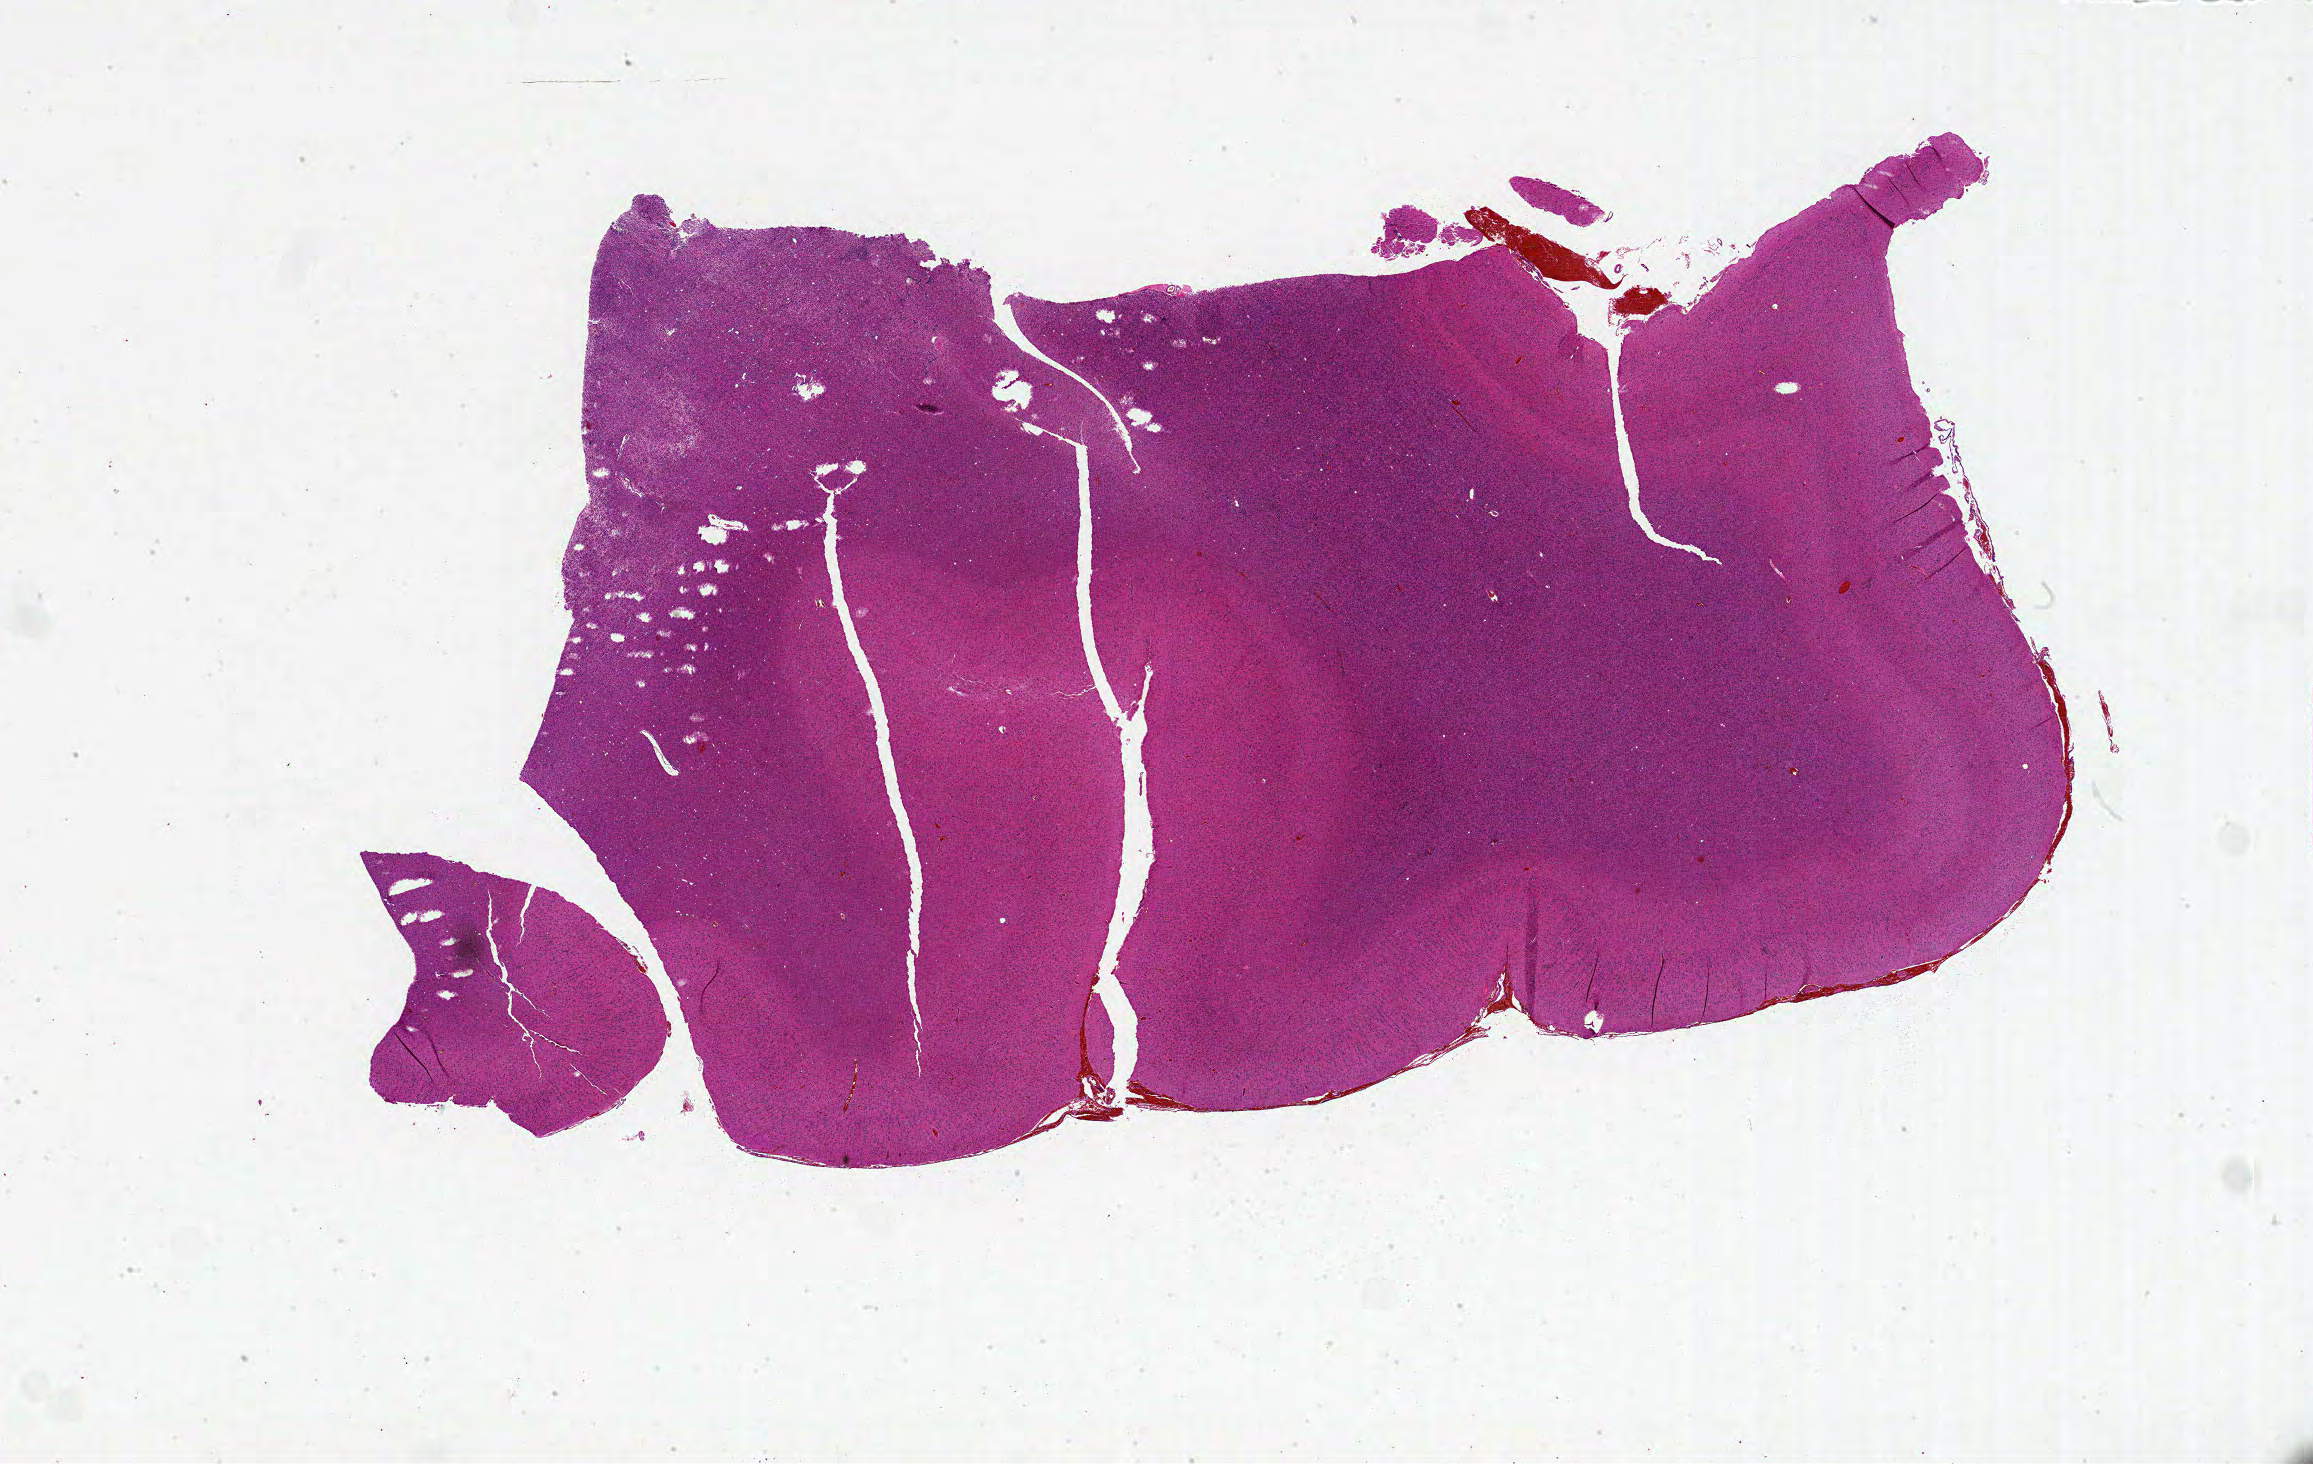
Whole-slide histology image, H&E-stained — shown as a low-resolution overview of the whole scanned area (about 37.0 x 23.4 mm, acquisition: 20x scan); formalin-fixed paraffin-embedded (FFPE) diagnostic section; brain, primary tumour sample. Male patient; age at initial diagnosis 77 years.
Diagnosis: Glioblastoma.